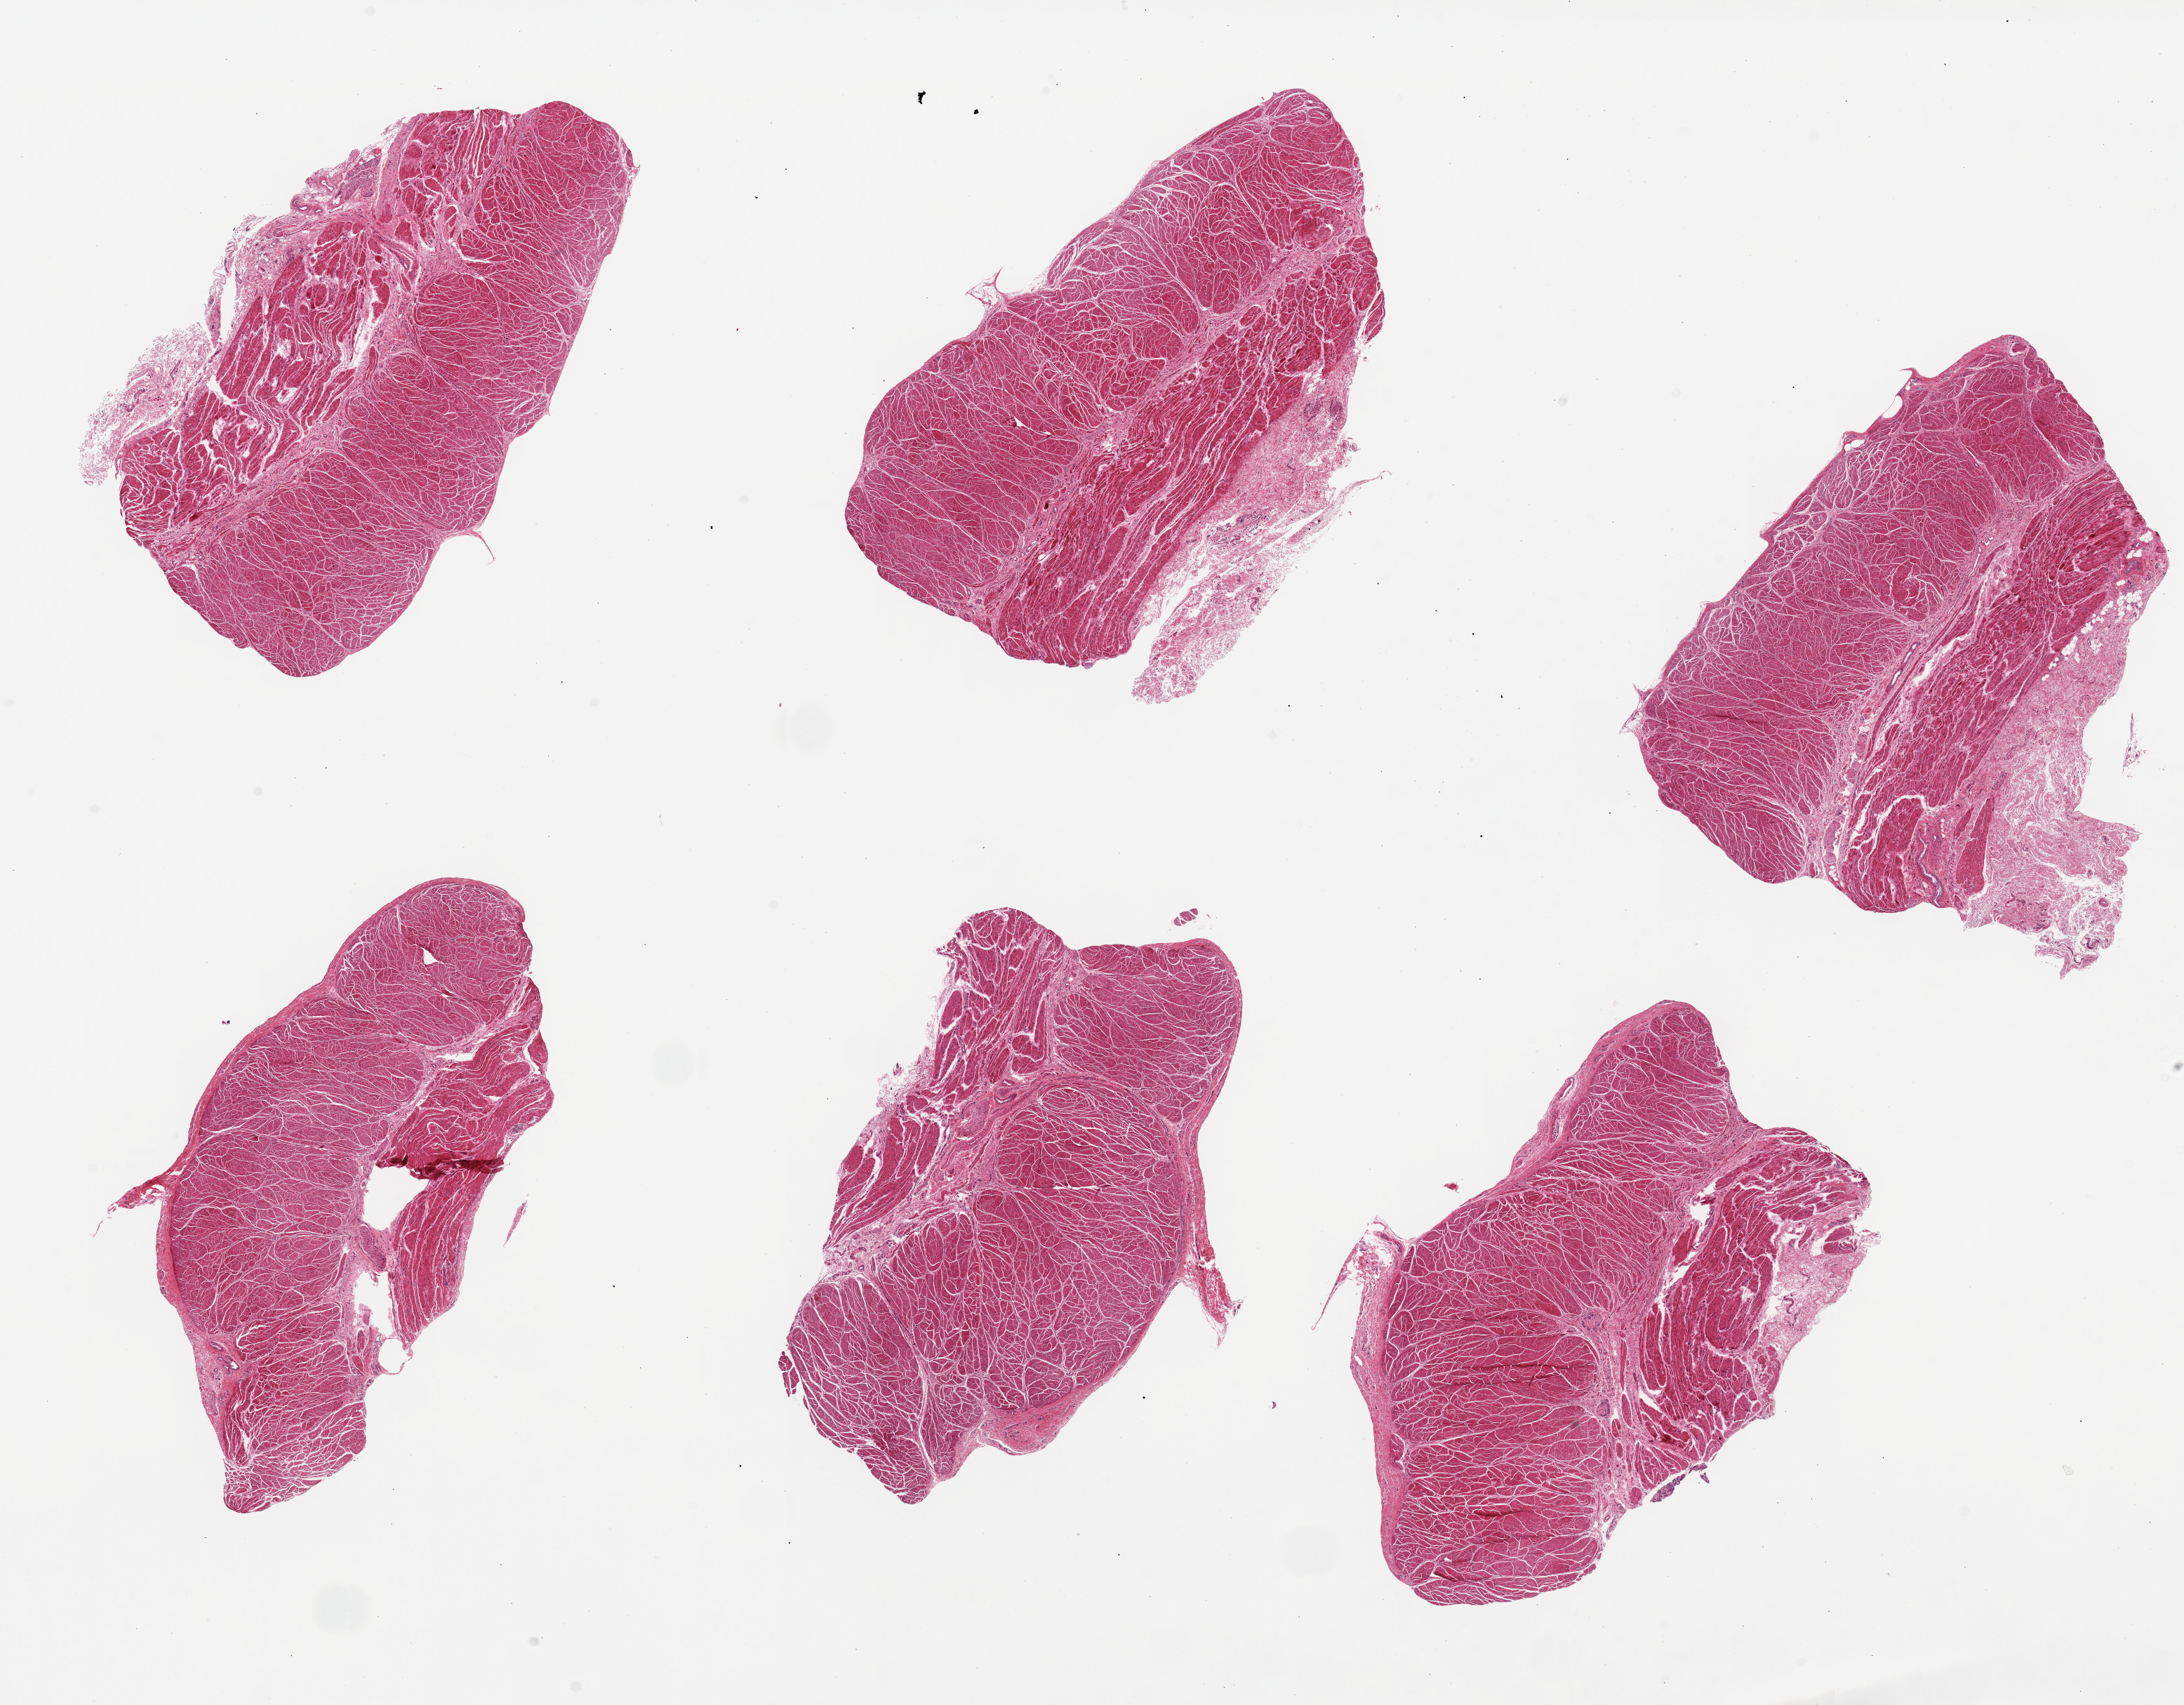
H&E whole-slide image — whole scanned area (about 24.6 x 19.2 mm, acquisition: 20x scan) shown as a low-resolution overview; PAXgene-fixed paraffin-embedded (PFPE) section; sampled site (target tissue): gastroesophageal junction; tissue donor sample. Female donor.
* review note (as recorded): 6 pieces, up to 7x5mm; 2 with 1mm extraneous stroma